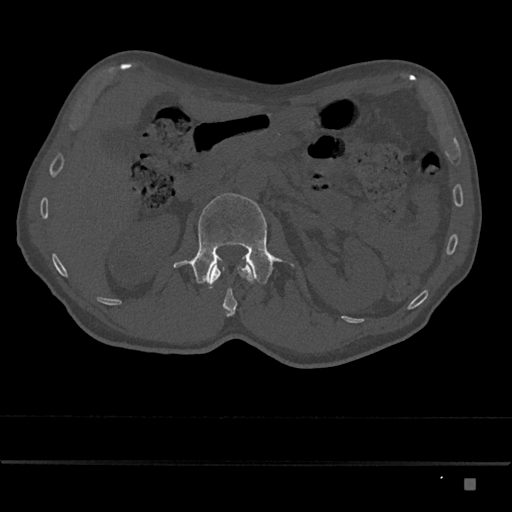
CT including the spine, one axial slice; slice 499 of 797 in the series (ordered by position); bone window (W 1800 / L 400 HU); 0.5 mm slice thickness; 512 × 512 image matrix, field of view 390 × 390 mm. Male patient, age 72 years. Case-level facts recorded for this patient, not image findings: primary cancer: prostate.
Annotated regions visible in this slice (semi-automatically segmented with operator editing):
- L1 vertebra: bounding box [x1, y1, x2, y2] px = [208, 257, 254, 317]
- L2 vertebra: [173, 193, 294, 285]